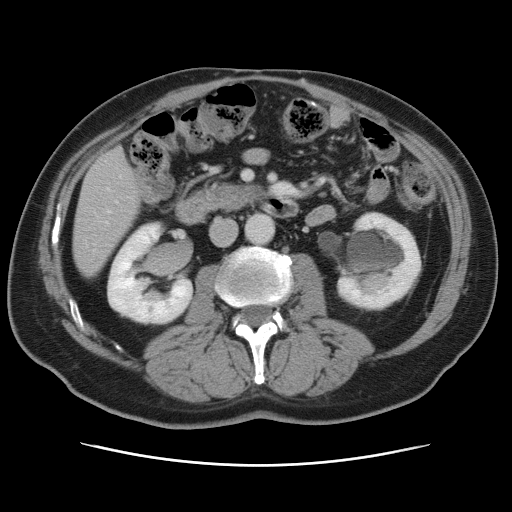
Contrast-enhanced abdominal CT, one axial slice; position 23 of 80 along the scan axis; intravenous contrast given; soft-tissue window (W 400 / L 40 HU); 512 × 512 image matrix. Male patient, age 69 years. From the clinical record (not read from this slice): diagnosis: colorectal cancer liver metastases, imaged before liver resection; multiple liver metastases: no; largest metastasis: 5 cm; disease in both lobes: yes.
Annotated regions visible in this slice (manually delineated by an expert):
- hepatic veins: bounding box [x1, y1, x2, y2] px = [107, 189, 117, 213]
- liver: [73, 150, 140, 276]
- planned liver remnant (the part of the liver to remain after resection): [74, 222, 124, 276]